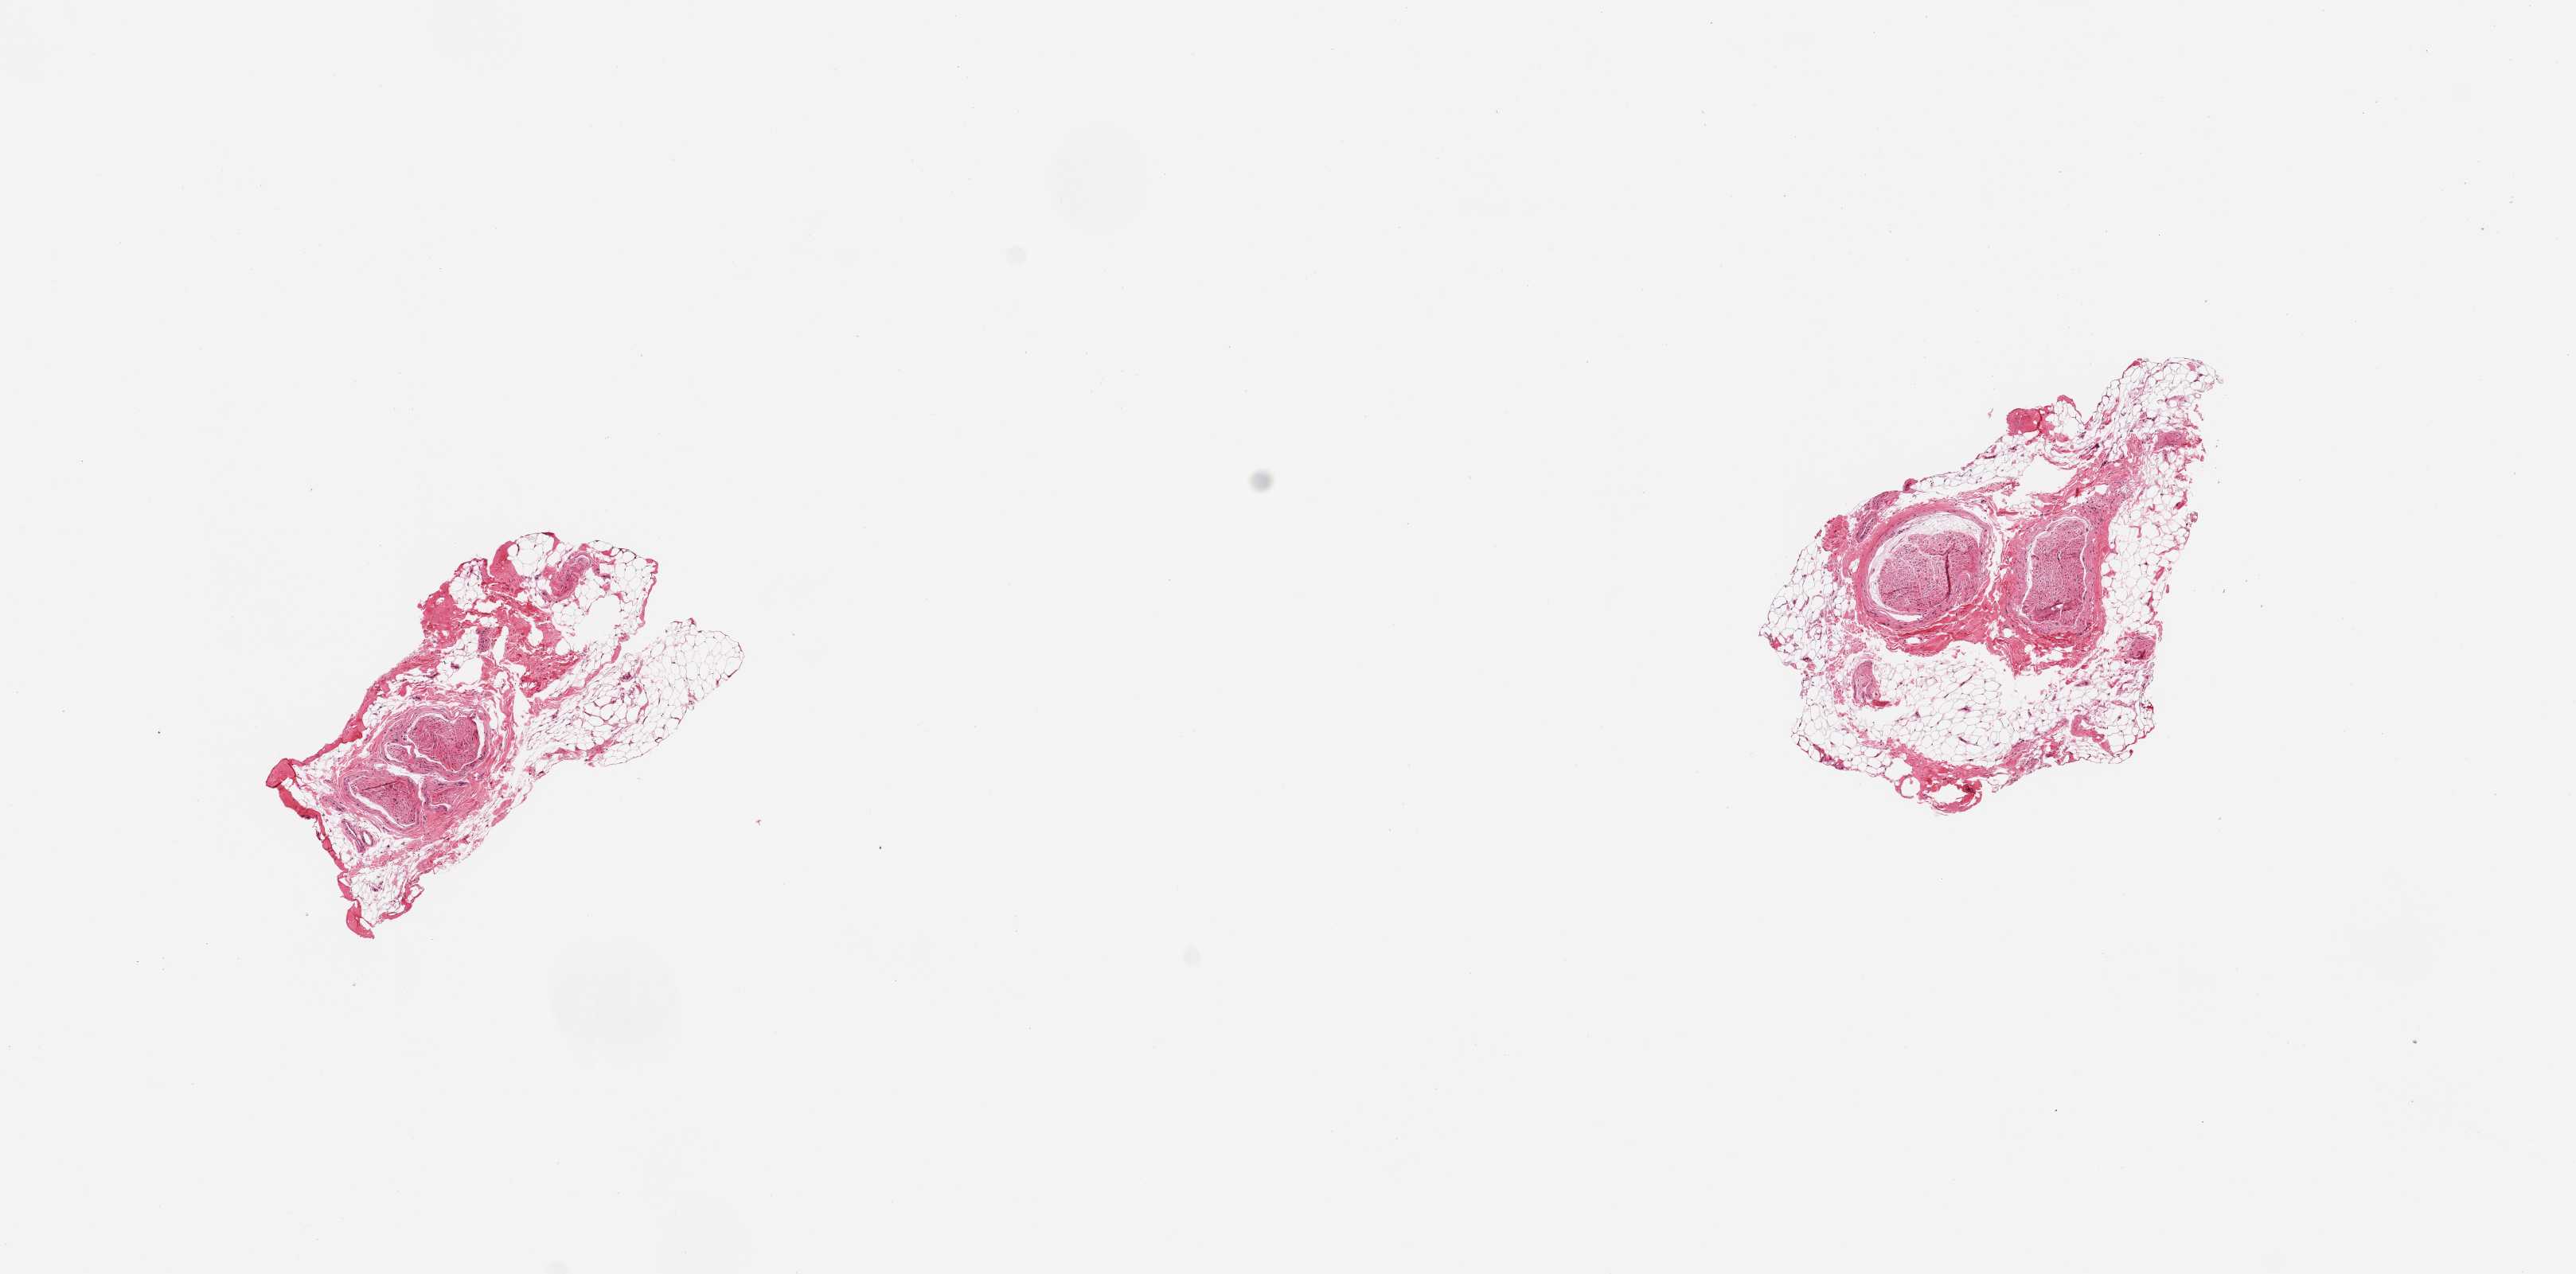
H&E whole-slide image — a low-resolution overview of the entire scanned area, about 12.8 x 6.3 mm (slide scanned at 20x). PAXgene-fixed paraffin-embedded (PFPE) section. Section of tibial nerve (target tissue). Donor tissue sample.
Pathologist's review note for this sample: 2 pieces; untrimmed nerve with 60% external fat.